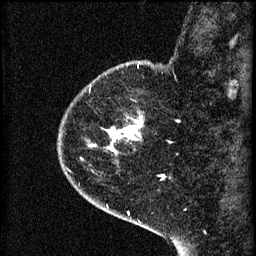
Breast MRI (dynamic contrast-enhanced), one sagittal slice. Position 13 of 60 along the scan axis. 3 images stored at this slice position (order not interpretable as contrast timing). 1.5 T. TE 4.2 ms, TR 8.2 ms. 2 mm slice thickness. 256 × 256 image matrix, field of view 180 × 180 mm. Female patient, age 44 years.
Outlined on this slice (semi-automatic segmentation, software-assisted and operator-edited):
- analysis volume of interest (the breast-tissue region the enhancement analysis was run in; not a lesion): bounding box <75,82,145,161> (left, top, right, bottom; pixels)
- tumour enhancement mask (voxels above the 70 % enhancement threshold inside the analysis volume of interest): <91,86,144,151>